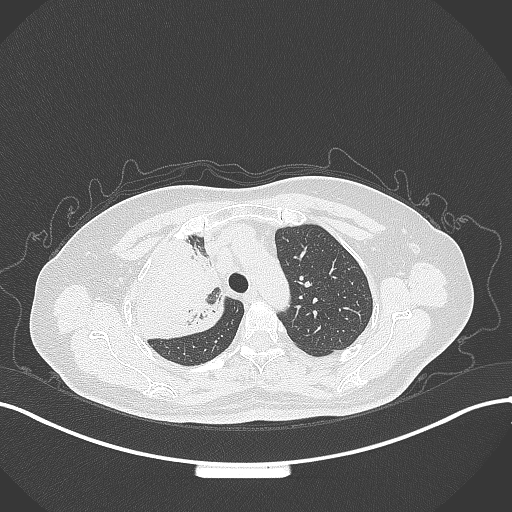
Chest CT, one axial slice; slice 241 of 309 in the series (ordered by position); reconstruction kernel B70f; lung window (W 1500 / L -600 HU); 1 mm slice thickness; 512 × 512 image matrix. Female patient, age 60 years. Case-level facts recorded for this patient, not image findings: clinical TNM (as recorded): T3 N1 M1.
Structures marked on this image (bounding box drawn by a radiologist):
- lung tumour (recorded histology: adenocarcinoma): bounding box [x1, y1, x2, y2] px = [124, 230, 234, 346]